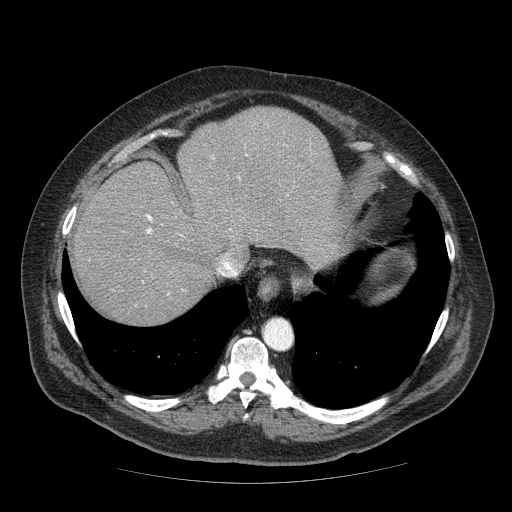
Contrast-enhanced abdominal CT (liver protocol), one axial slice. Position 56 of 85 along the scan axis. Soft-tissue window (W 400 / L 40 HU). 512 × 512 image matrix, field of view 420 × 420 mm. Case-level facts recorded for this patient, not image findings: diagnosis: hepatocellular carcinoma (patient treated with transarterial chemoembolisation; whether this scan precedes or follows treatment is not stated here); TNM stage (as recorded): Stage-IIIA; Child-Pugh class: A; tumour nodularity: multinodular.
Outlined on this slice (semi-automatic segmentation, software-assisted and operator-edited):
- abdominal aorta: bounding box [x1, y1, x2, y2] px = [264, 320, 293, 350]
- liver parenchyma outside the tumour (the mass and vessels are separate outlines, so this box may not span the whole liver): [72, 106, 344, 324]
- liver vessels: [146, 178, 240, 236]